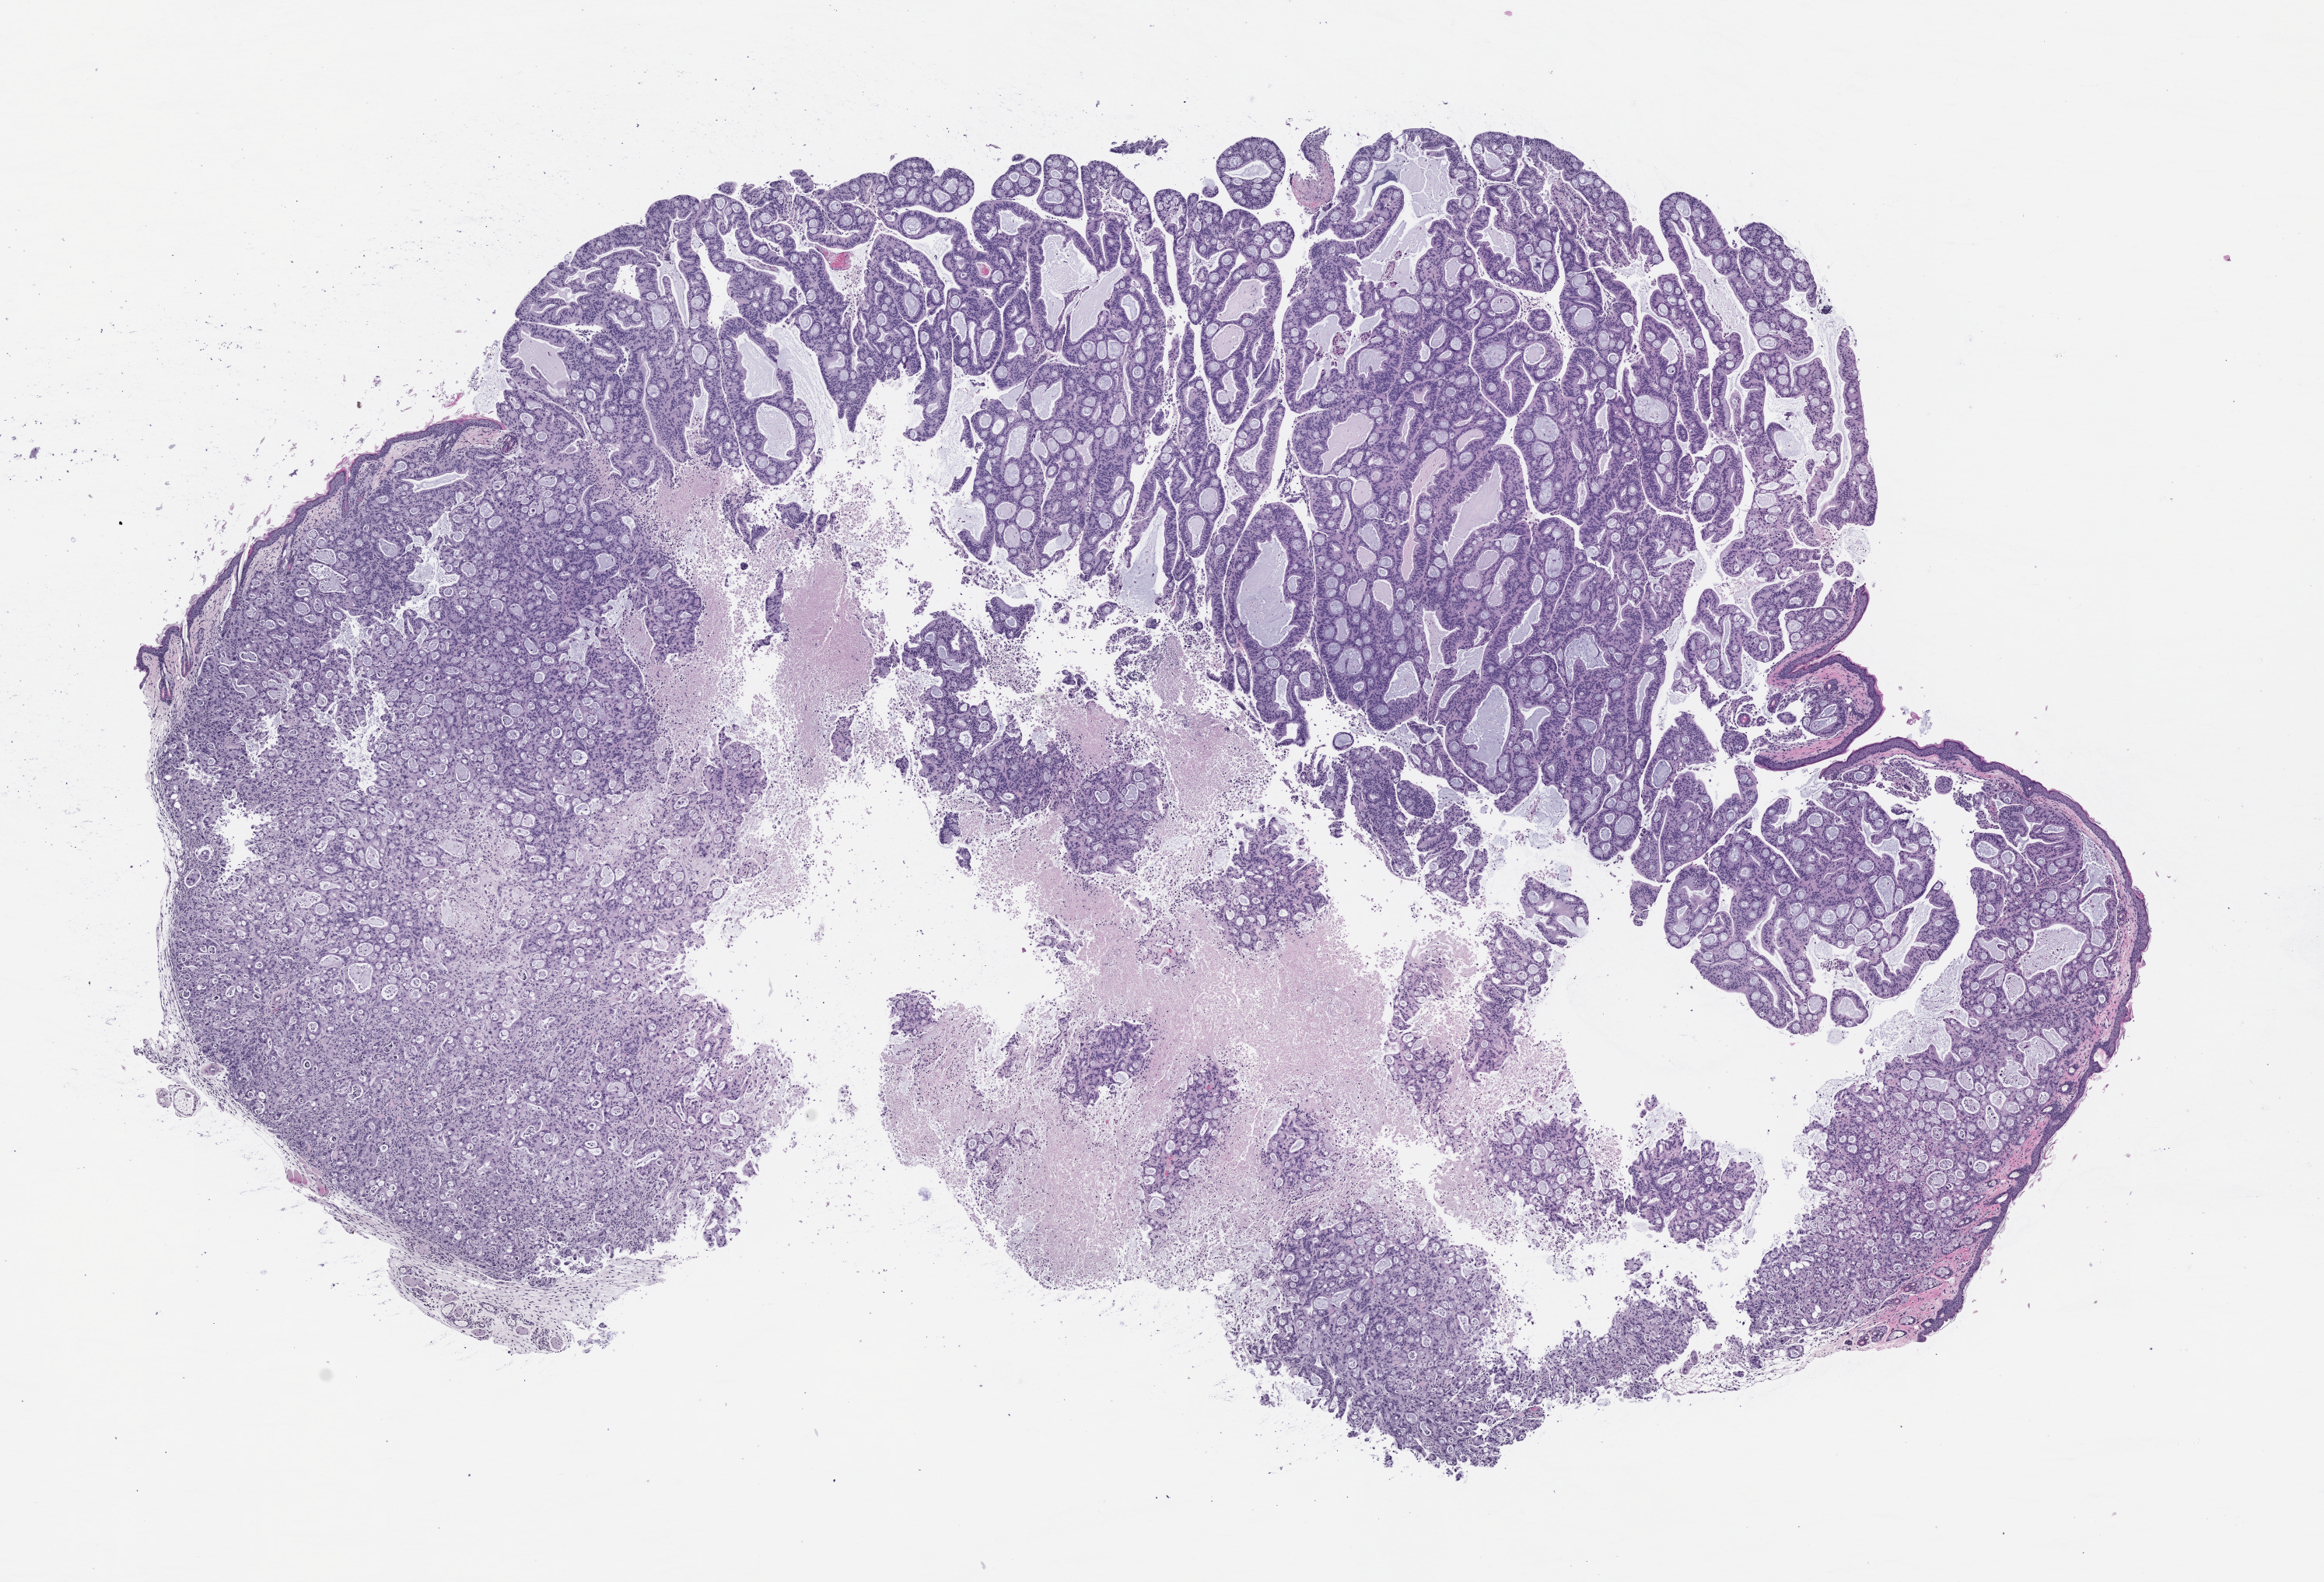
H&E whole-slide image of a patient-derived xenograft (PDX) tumor grown in a mouse — a low-resolution overview of the entire scanned area, about 12.0 x 8.2 mm. Formalin-fixed paraffin-embedded section. Originating tumor site category: pancreas.
* originating patient diagnosis: Pancreatic Adenocarcinoma